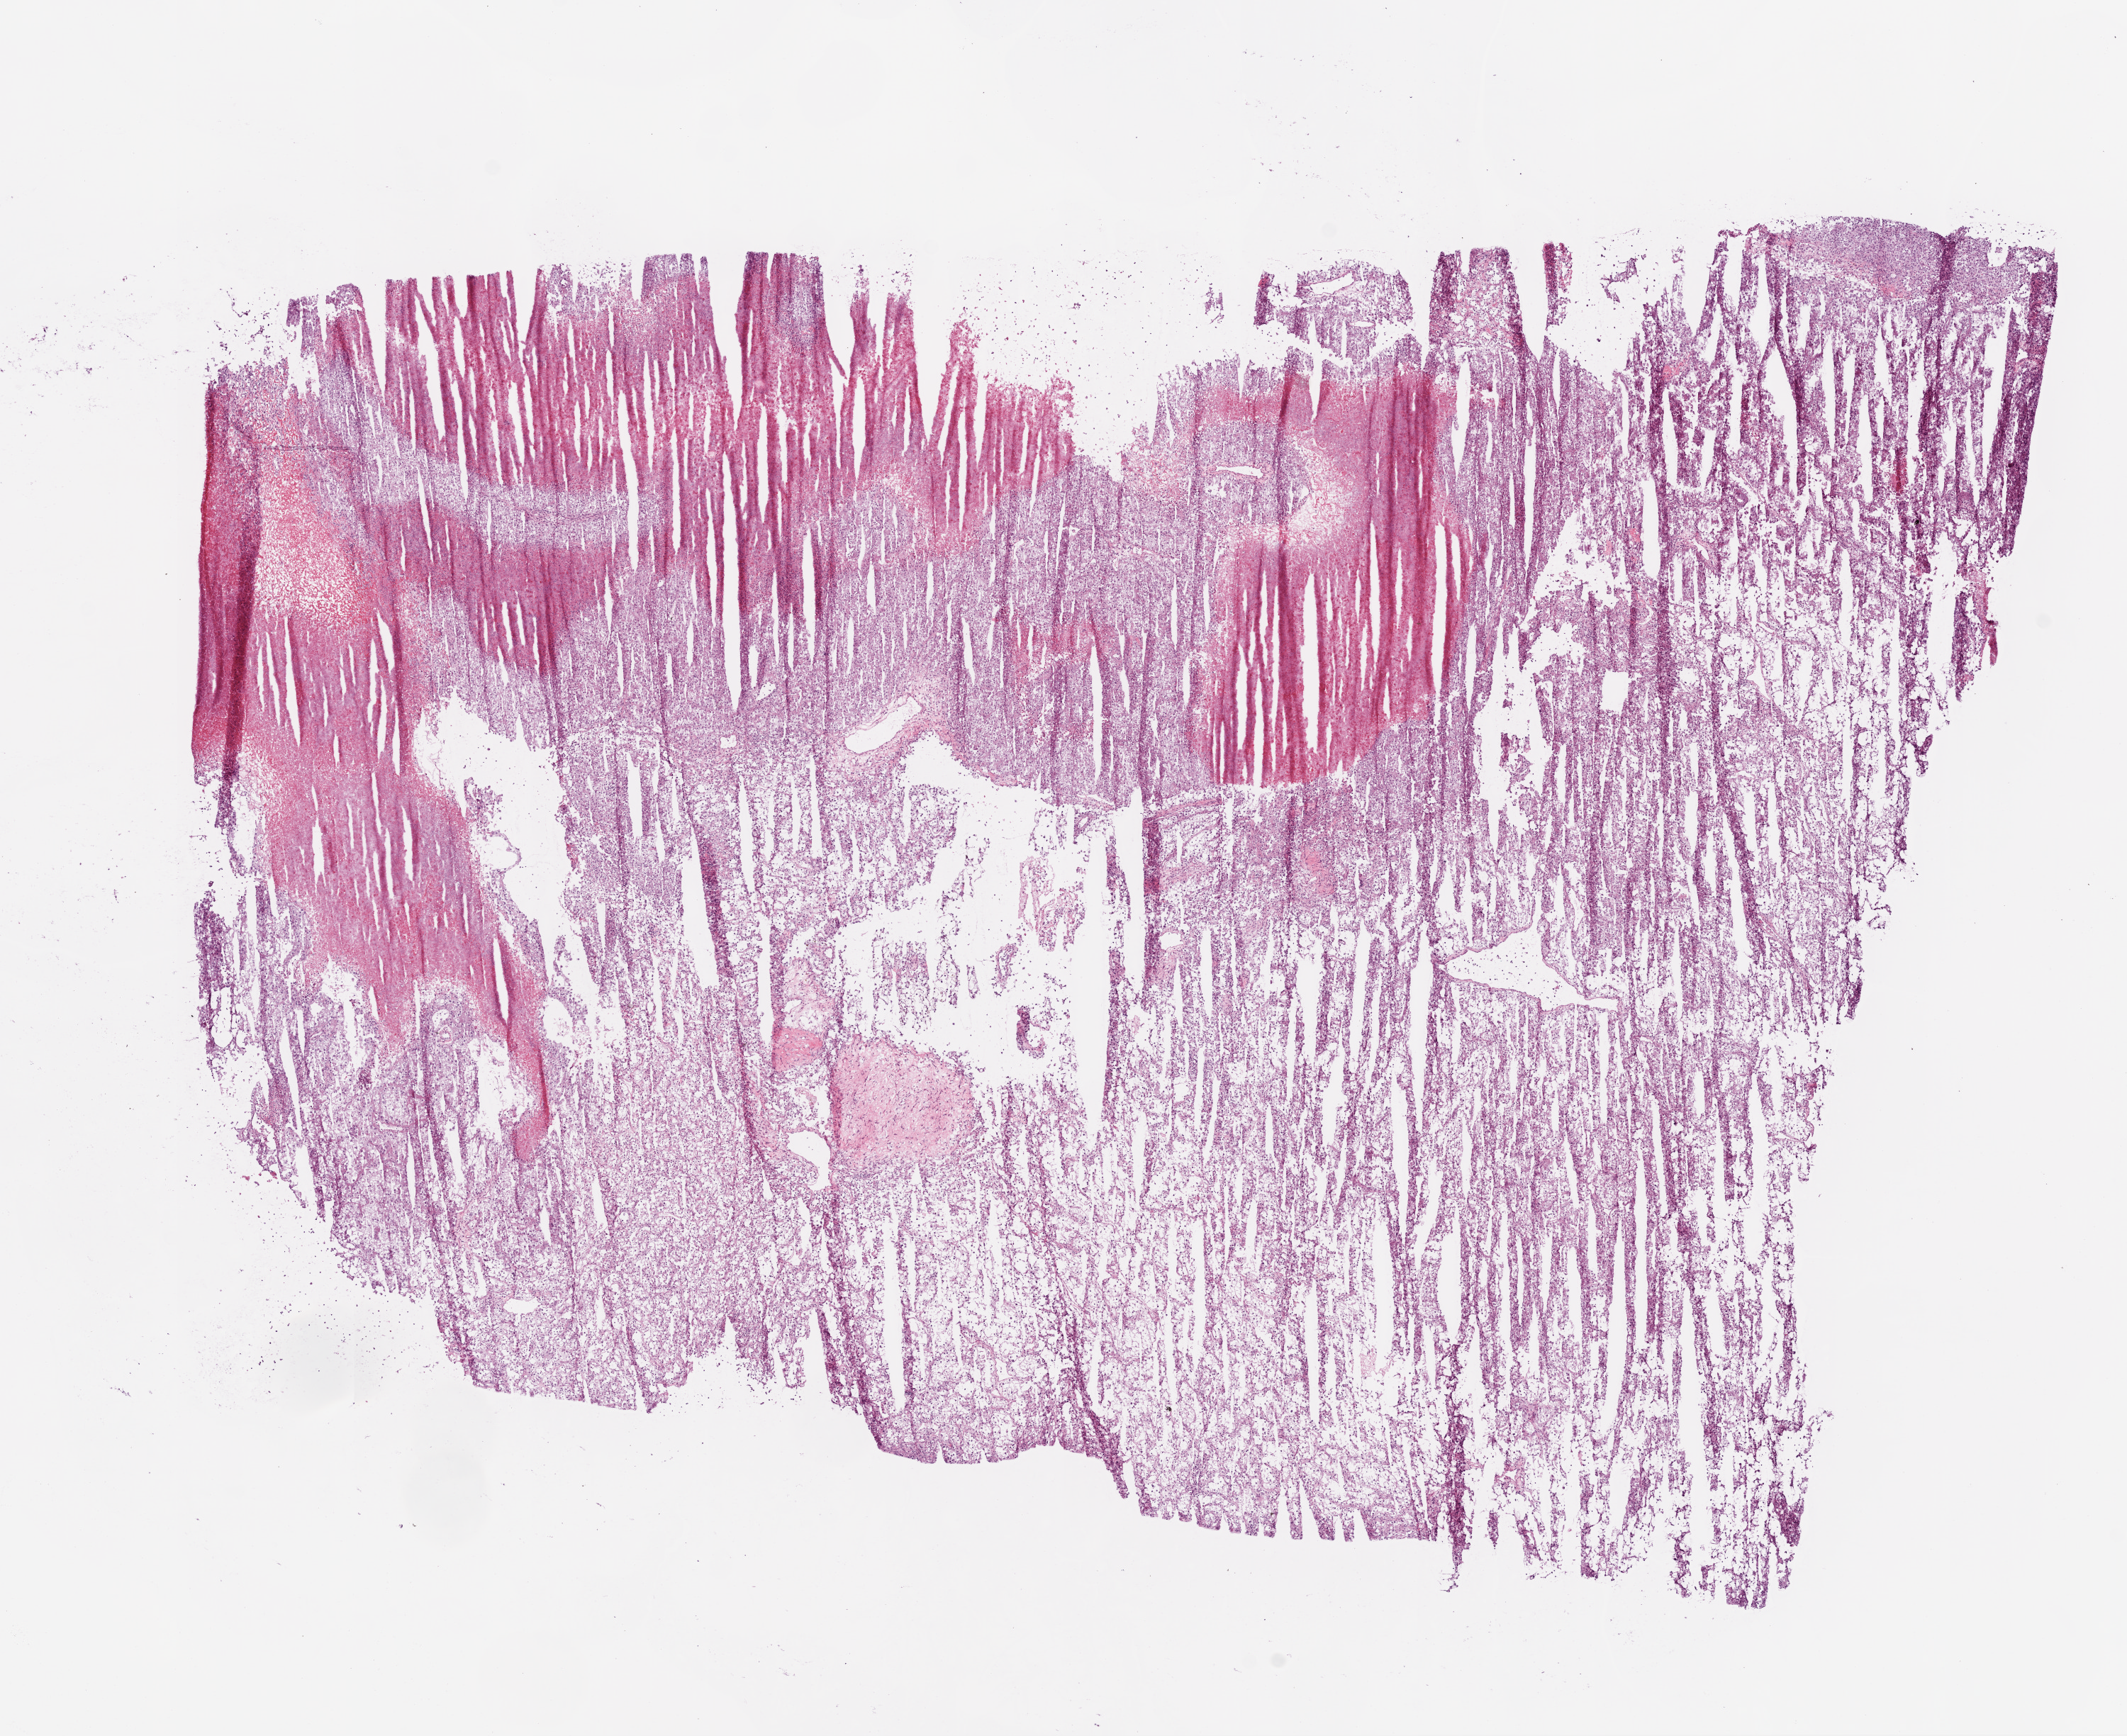
Whole-slide histology image, H&E — a low-resolution overview of the entire scanned area, about 12.0 x 9.8 mm; frozen section from the top of the tissue portion; sample: primary tumour, kidney. Male patient; age at initial diagnosis 56 years. Histologic grade: G4 (undifferentiated). Composition of this section per pathologist review: tumour cells 75%, tumour nuclei 85%, normal cells 0%, stromal cells 5%, necrosis 20%.
- histologic diagnosis: Clear cell adenocarcinoma, NOS
- laterality: left
- AJCC pathologic stage: III